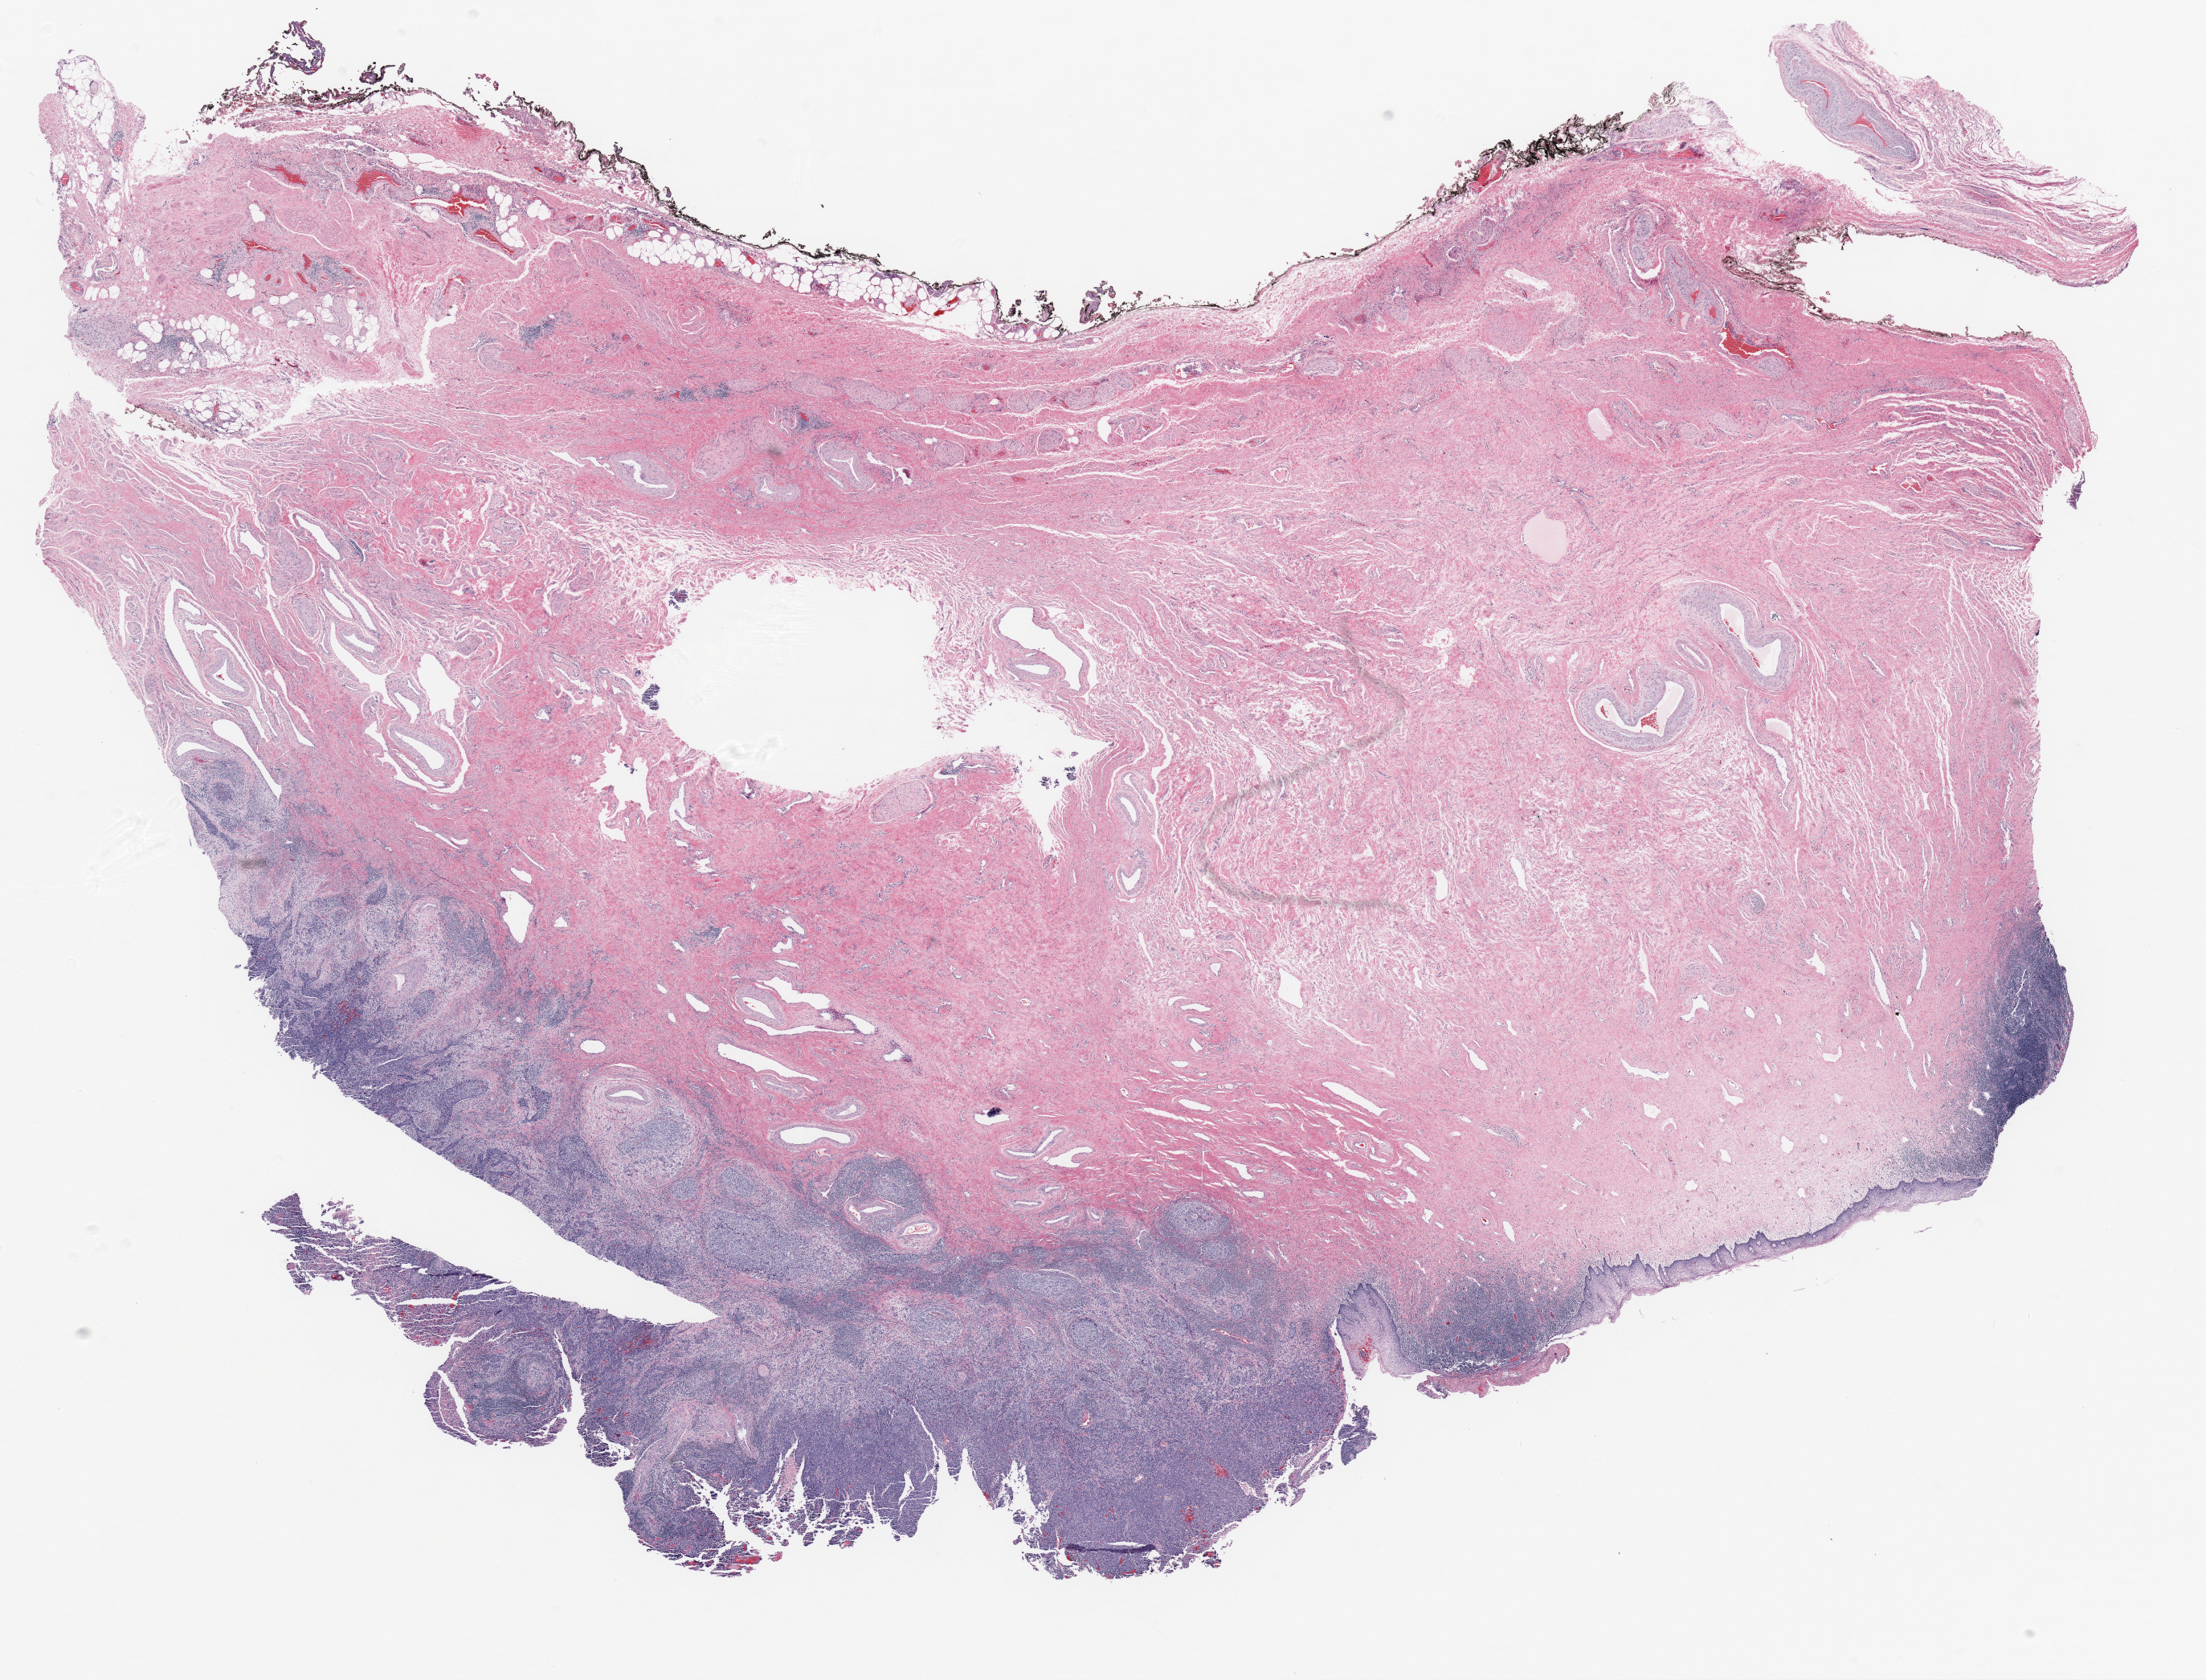
Whole-slide histology image, H&E-stained — low-resolution overview of the scanned area, about 21.9 x 16.7 mm. FFPE section. Cervix, primary tumour sample. Female, age 49 years at initial diagnosis. Histologic grade: G4 (undifferentiated).
* pathologic diagnosis: Squamous cell carcinoma, NOS (cervix uteri)
* FIGO stage: IIA1